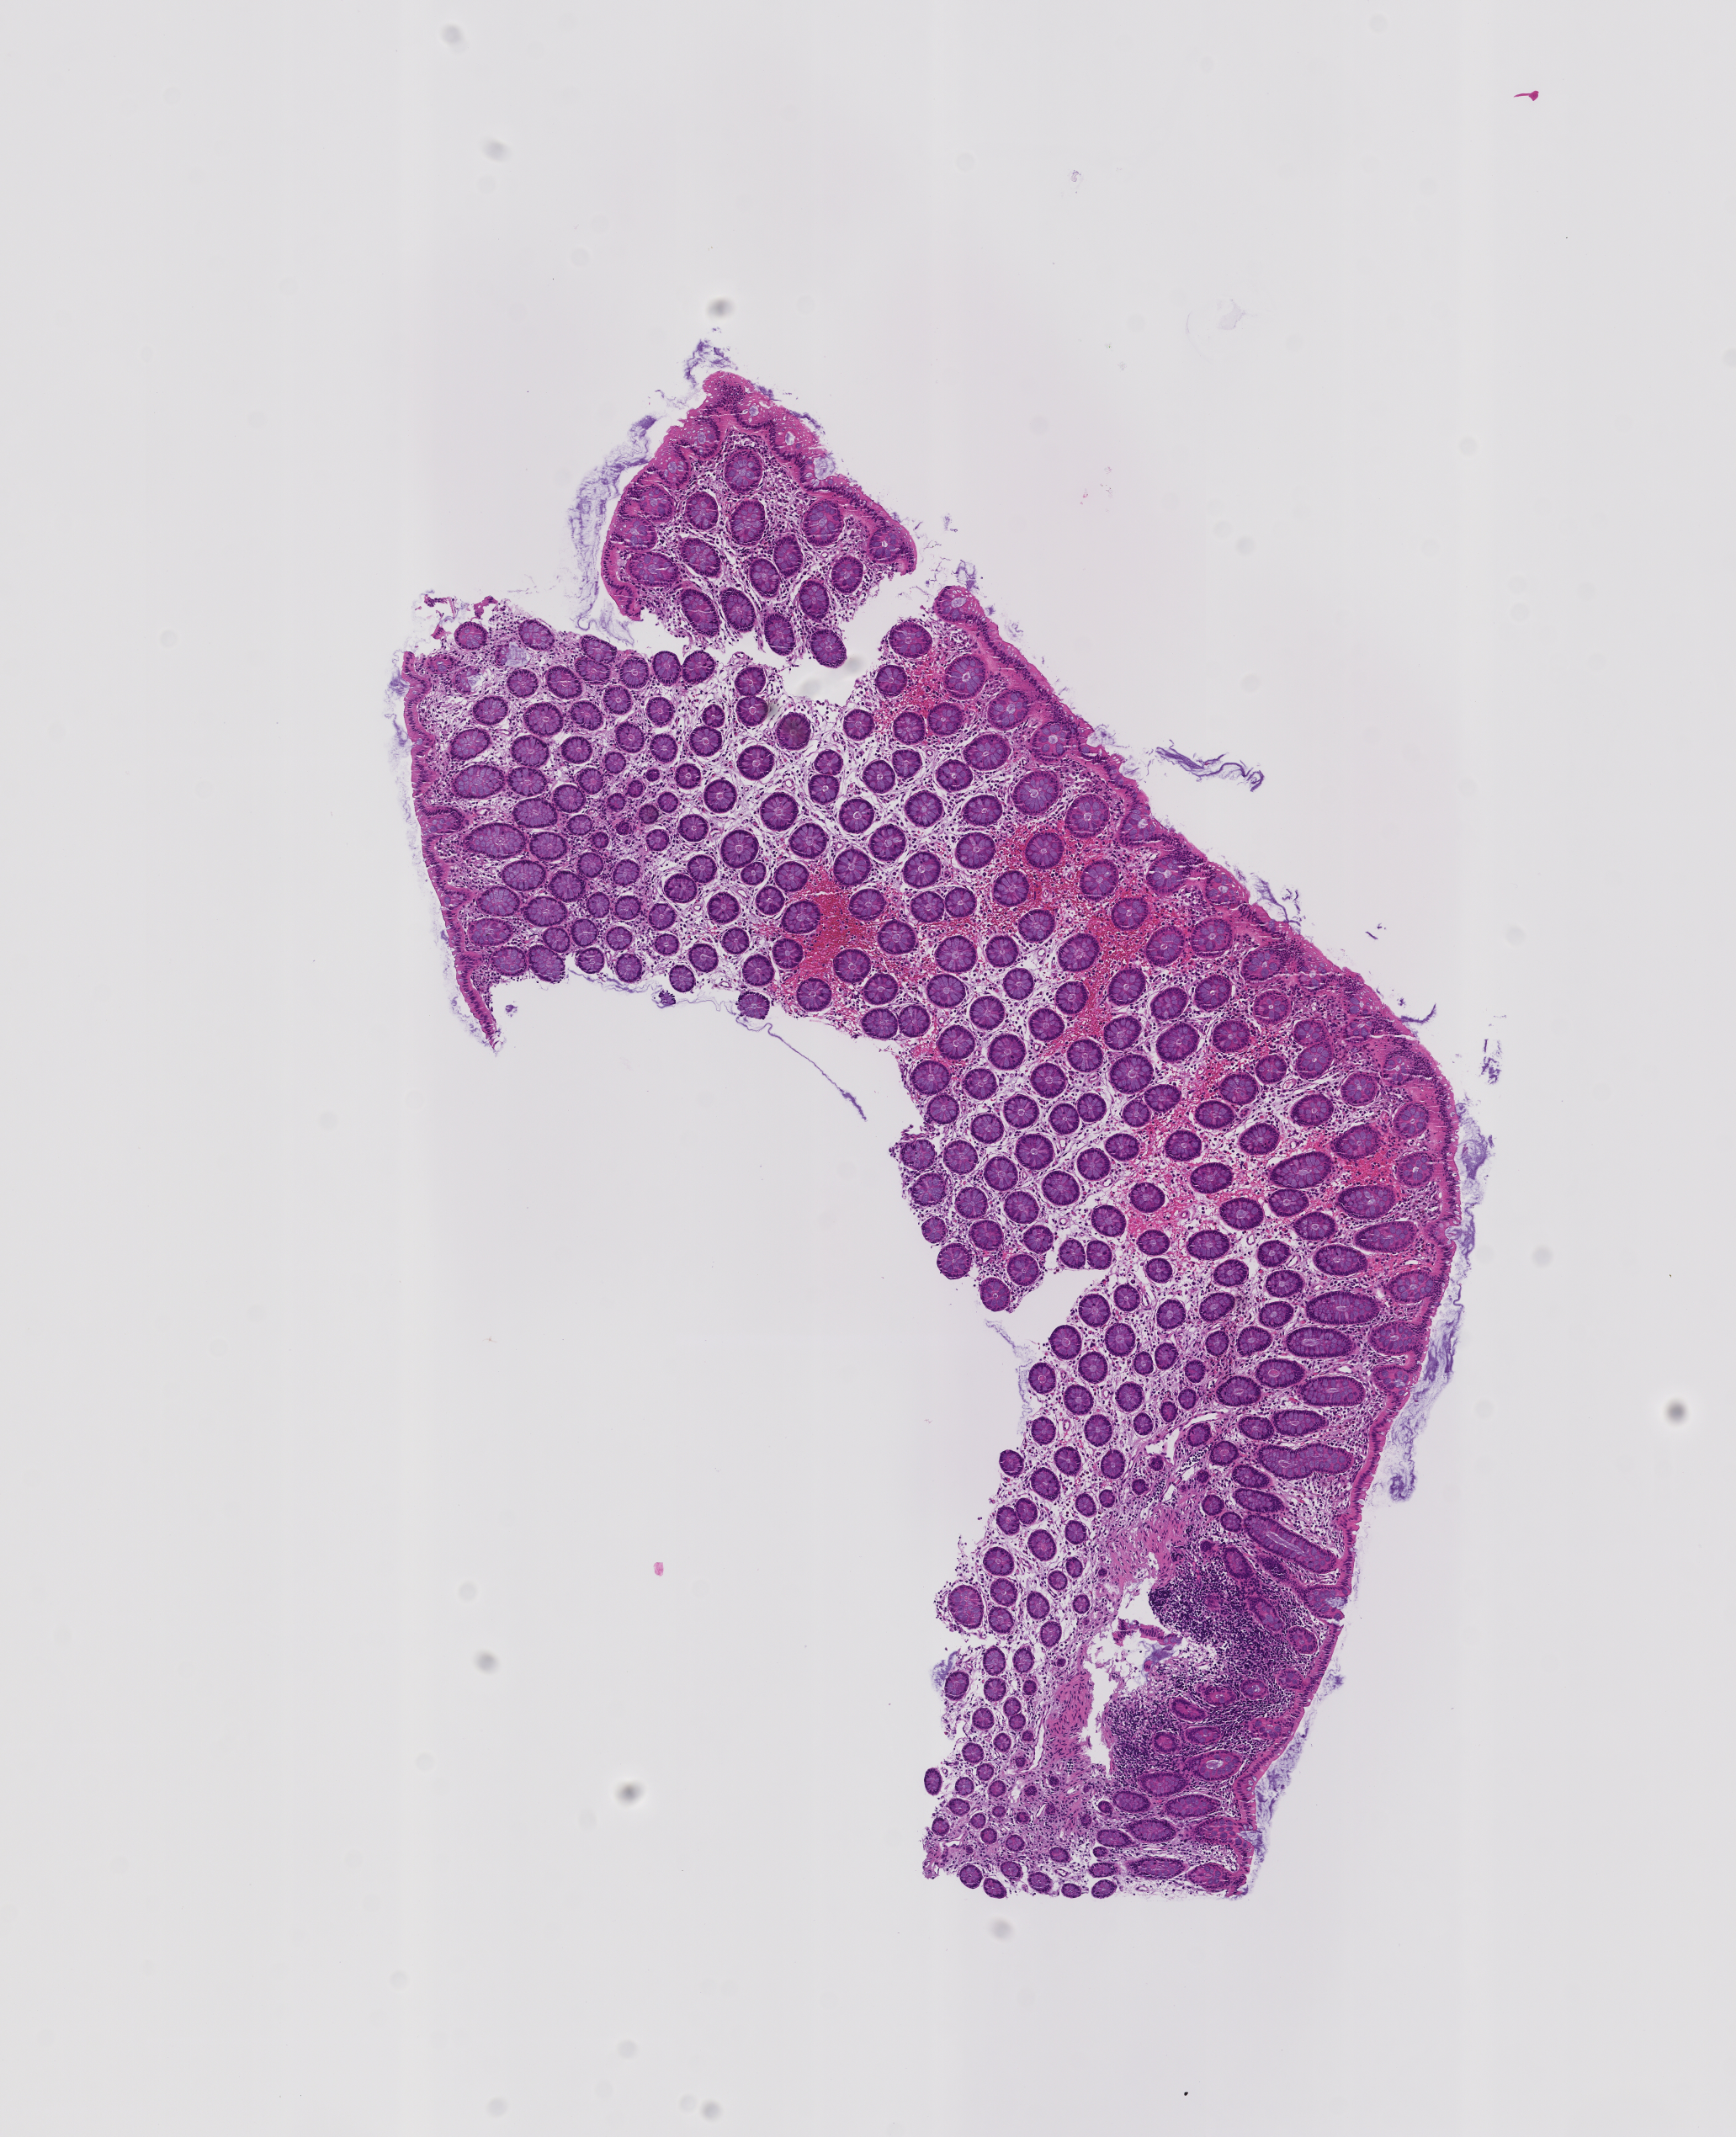
Haematoxylin and eosin whole-slide image of a colon biopsy, low-resolution overview of the scanned area, about 4.1 x 5.1 mm; formalin-fixed paraffin-embedded section; transverse colon. Patient sex: female.
Lesion category (as recorded): normal (as recorded).